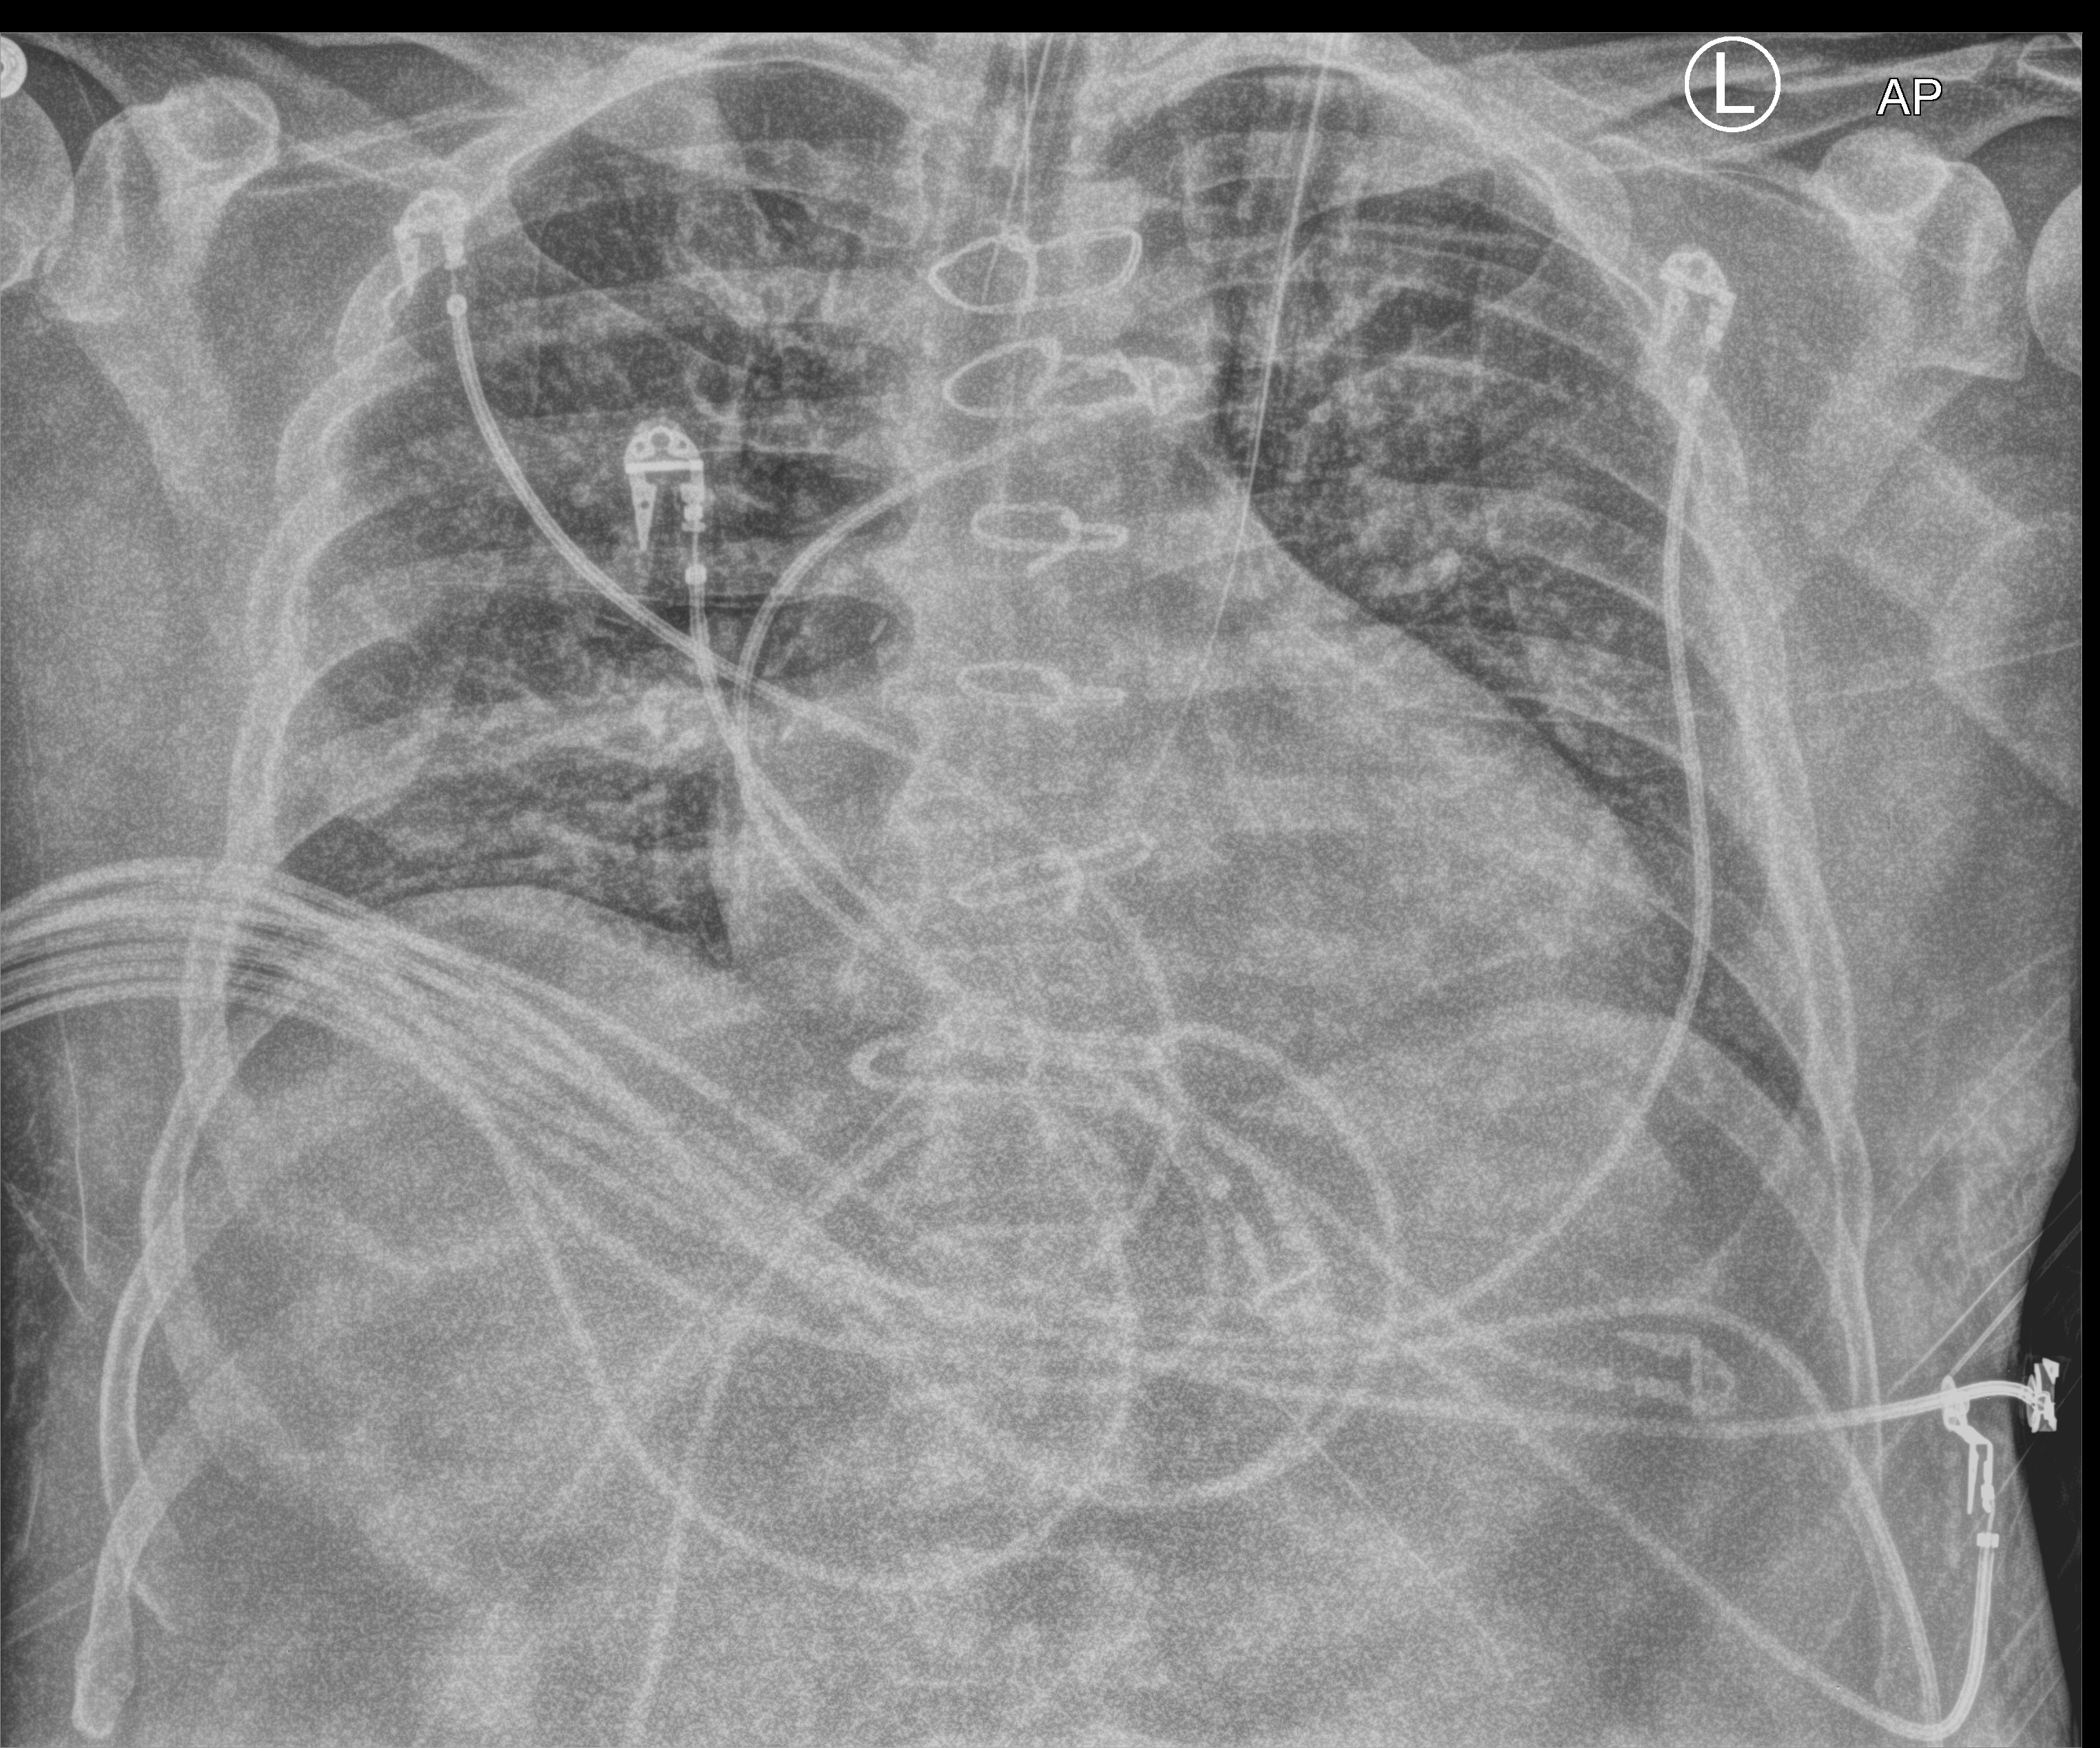
Bedside chest radiograph (computed radiography). Adult patient hospitalised with COVID-19, age 18–59 years.
From the hospital-stay record, not from the radiograph (when in the stay this image was taken is not recorded): admitted to intensive care during this hospital stay: yes; mechanically ventilated during this hospital stay: yes.